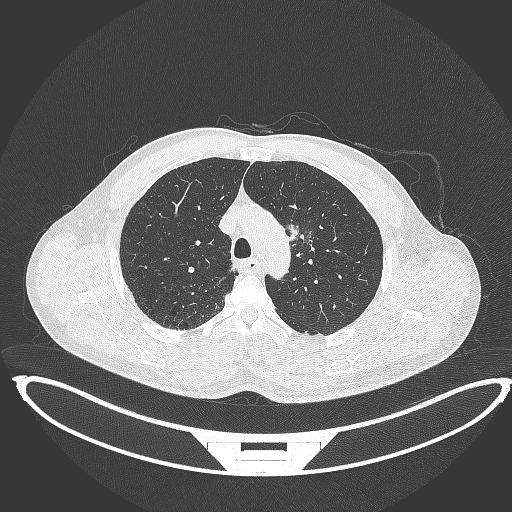
Chest CT, one axial slice; slice 329 of 395 in the series (ordered by position); lung window (W 1500 / L -600 HU); 512 × 512 image matrix, field of view 457 × 457 mm. Male patient, age 60 years. From the clinical record (not read from this slice): clinical TNM (as recorded): T2a N0 M0; histopathological grade: G1-G2.
Outlined on this slice (rectangle marked by the reading radiologist):
- lung tumour (recorded histology: squamous cell carcinoma): bounding box (x1, y1, x2, y2) in pixels: (285, 218, 302, 244)